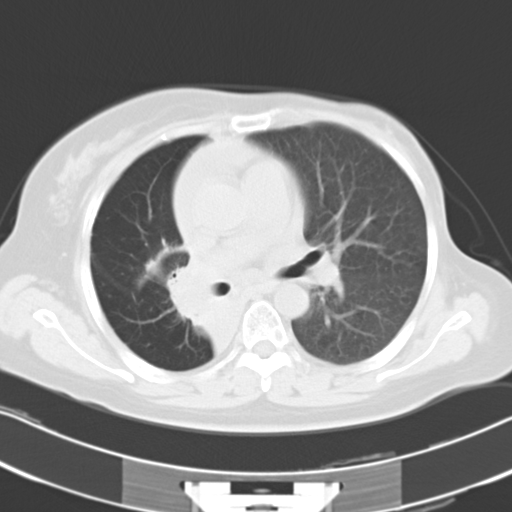
Chest CT, one axial slice; position 18 of 30 along the scan axis; 120 kVp; lung window (W 1500 / L -600 HU); 512 × 512 image matrix. Female patient, age 53 years. Case-level facts recorded for this patient, not image findings: clinical TNM (as recorded): T2b N1 M0.
Structures marked on this image (bounding box drawn by a radiologist):
- lung tumour (recorded histology: adenocarcinoma): bounding box (x1, y1, x2, y2) in pixels: (160, 255, 217, 330)